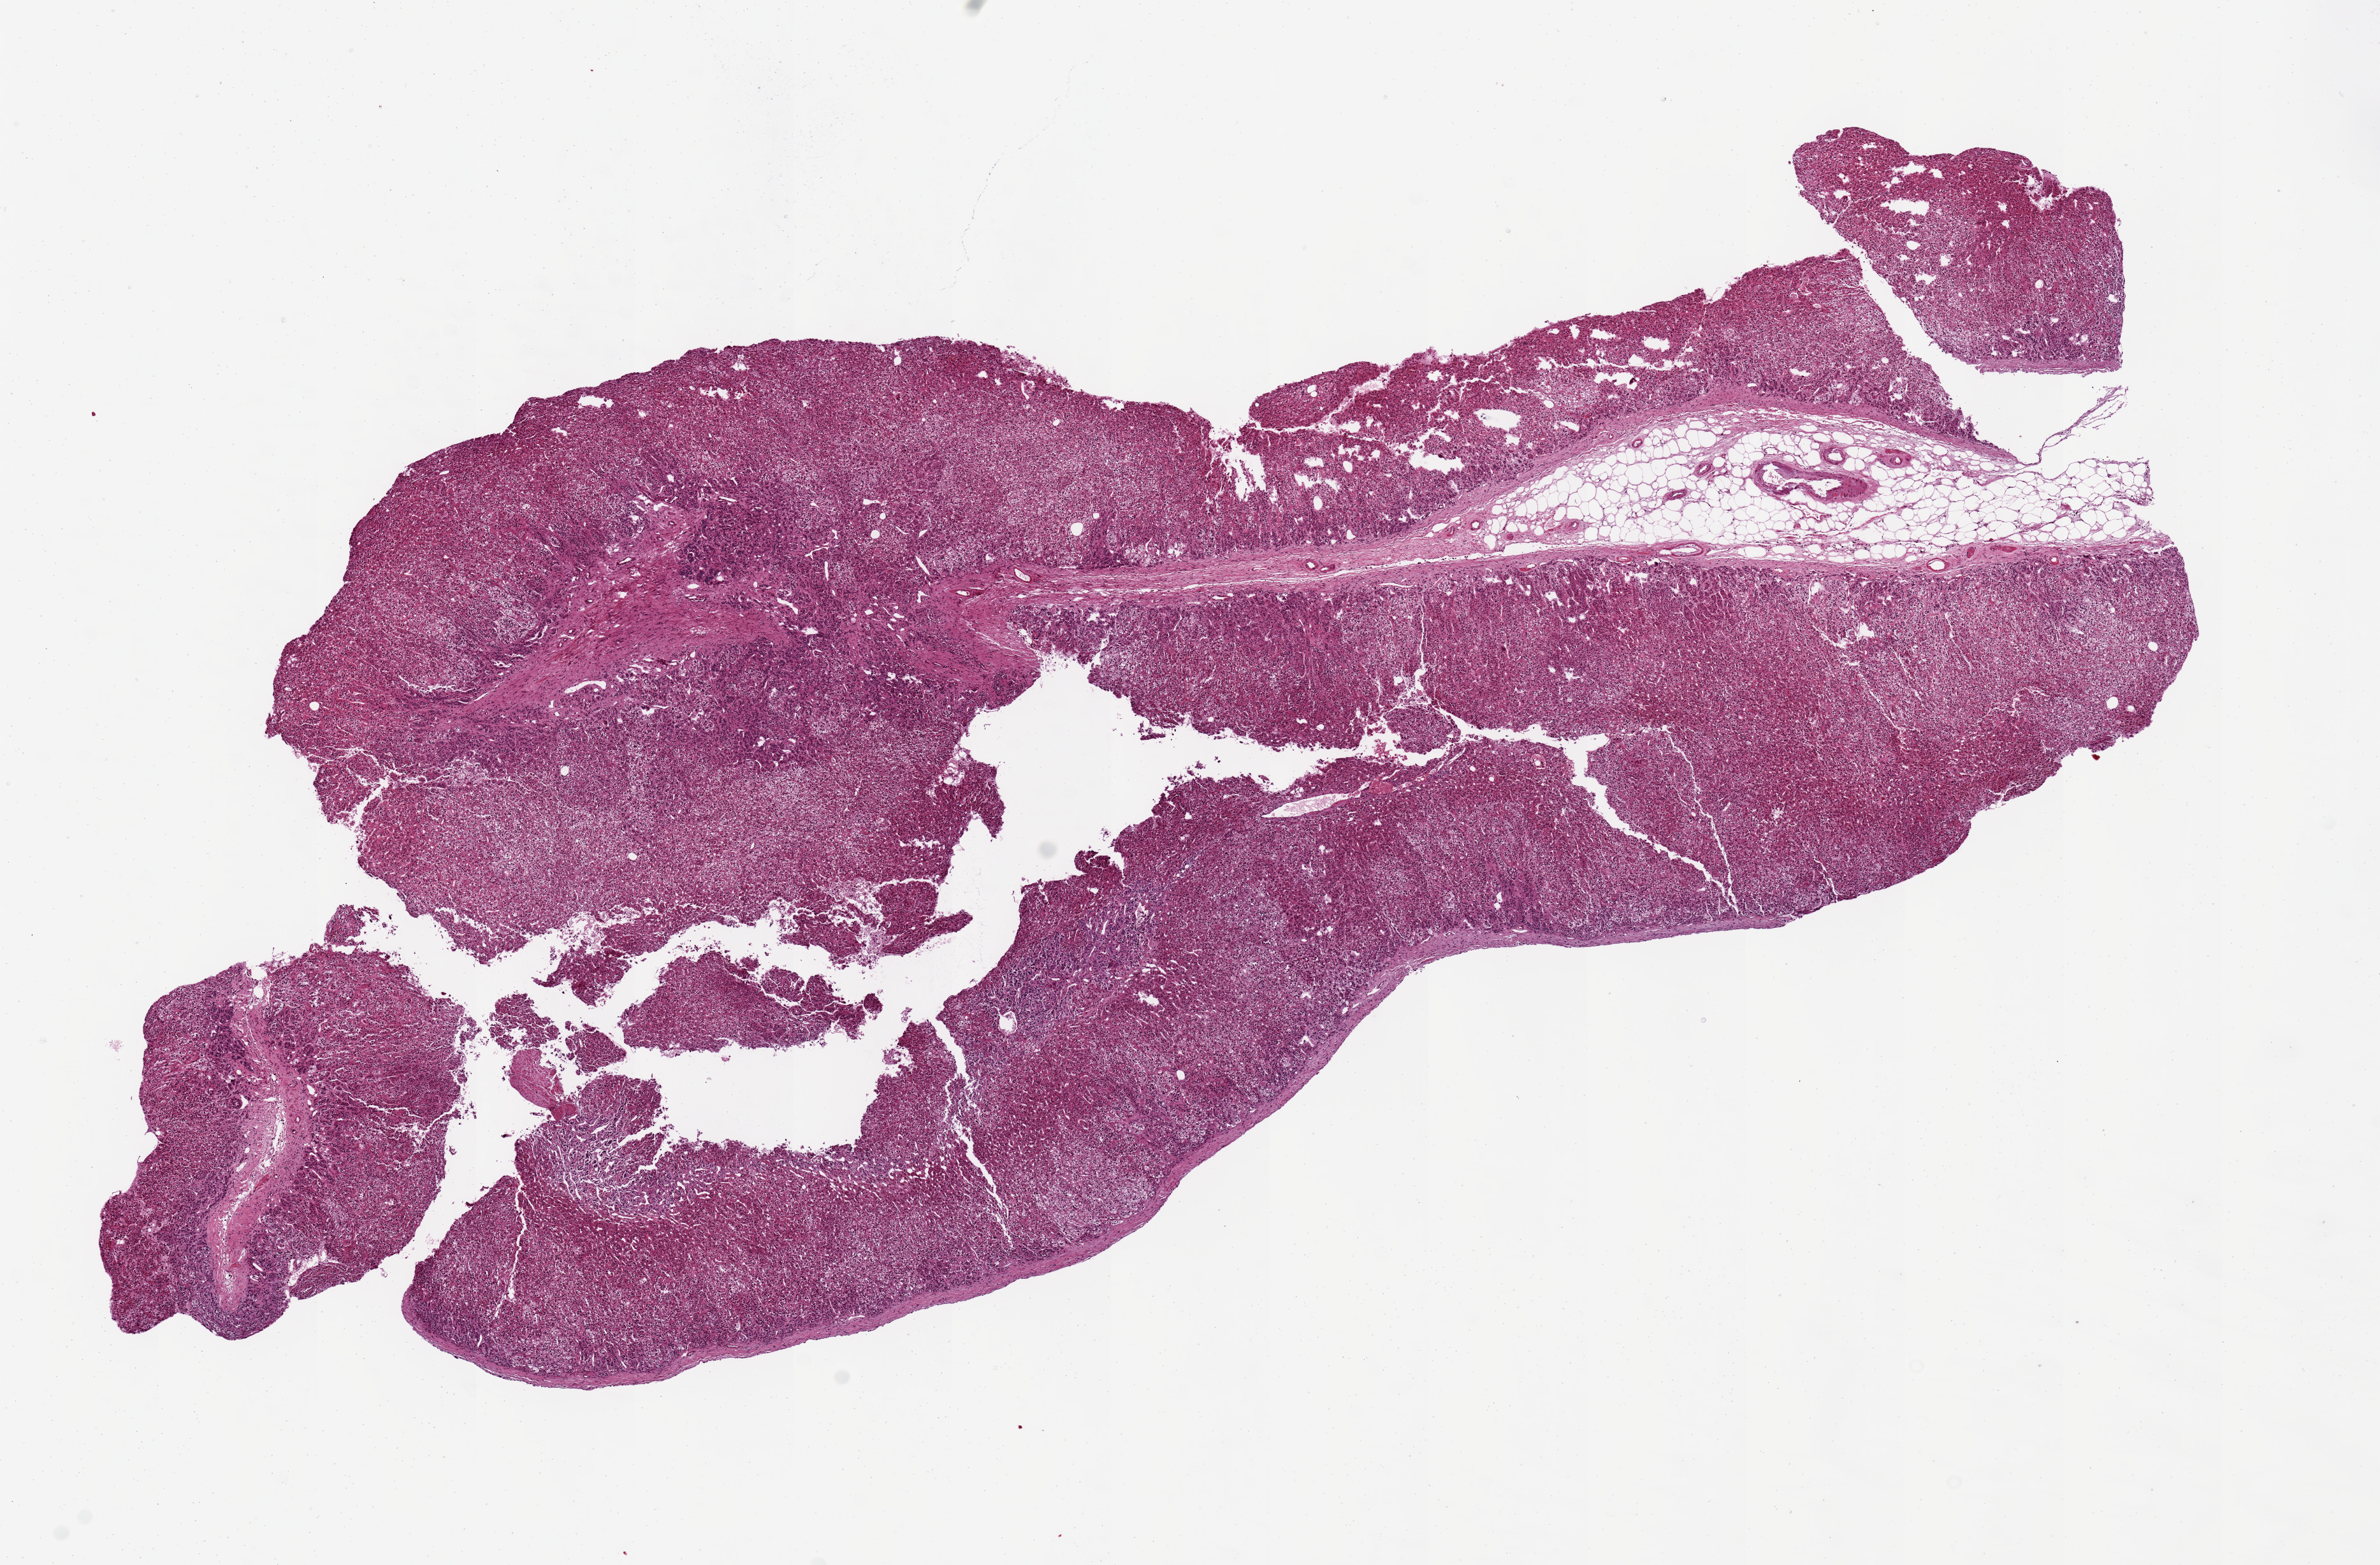
Digitized hematoxylin and eosin (H&E)-stained section, shown as a low-resolution overview of the whole scanned area (about 14.8 x 9.7 mm, slide scanned at 20x), PAXgene-fixed paraffin-embedded (PFPE) section, sampled site (target tissue): adrenal gland, donor tissue sample. Donor: male.
Pathologist's review note for this sample: Cortex is ~95% of specimen, rest is adipose tissue.